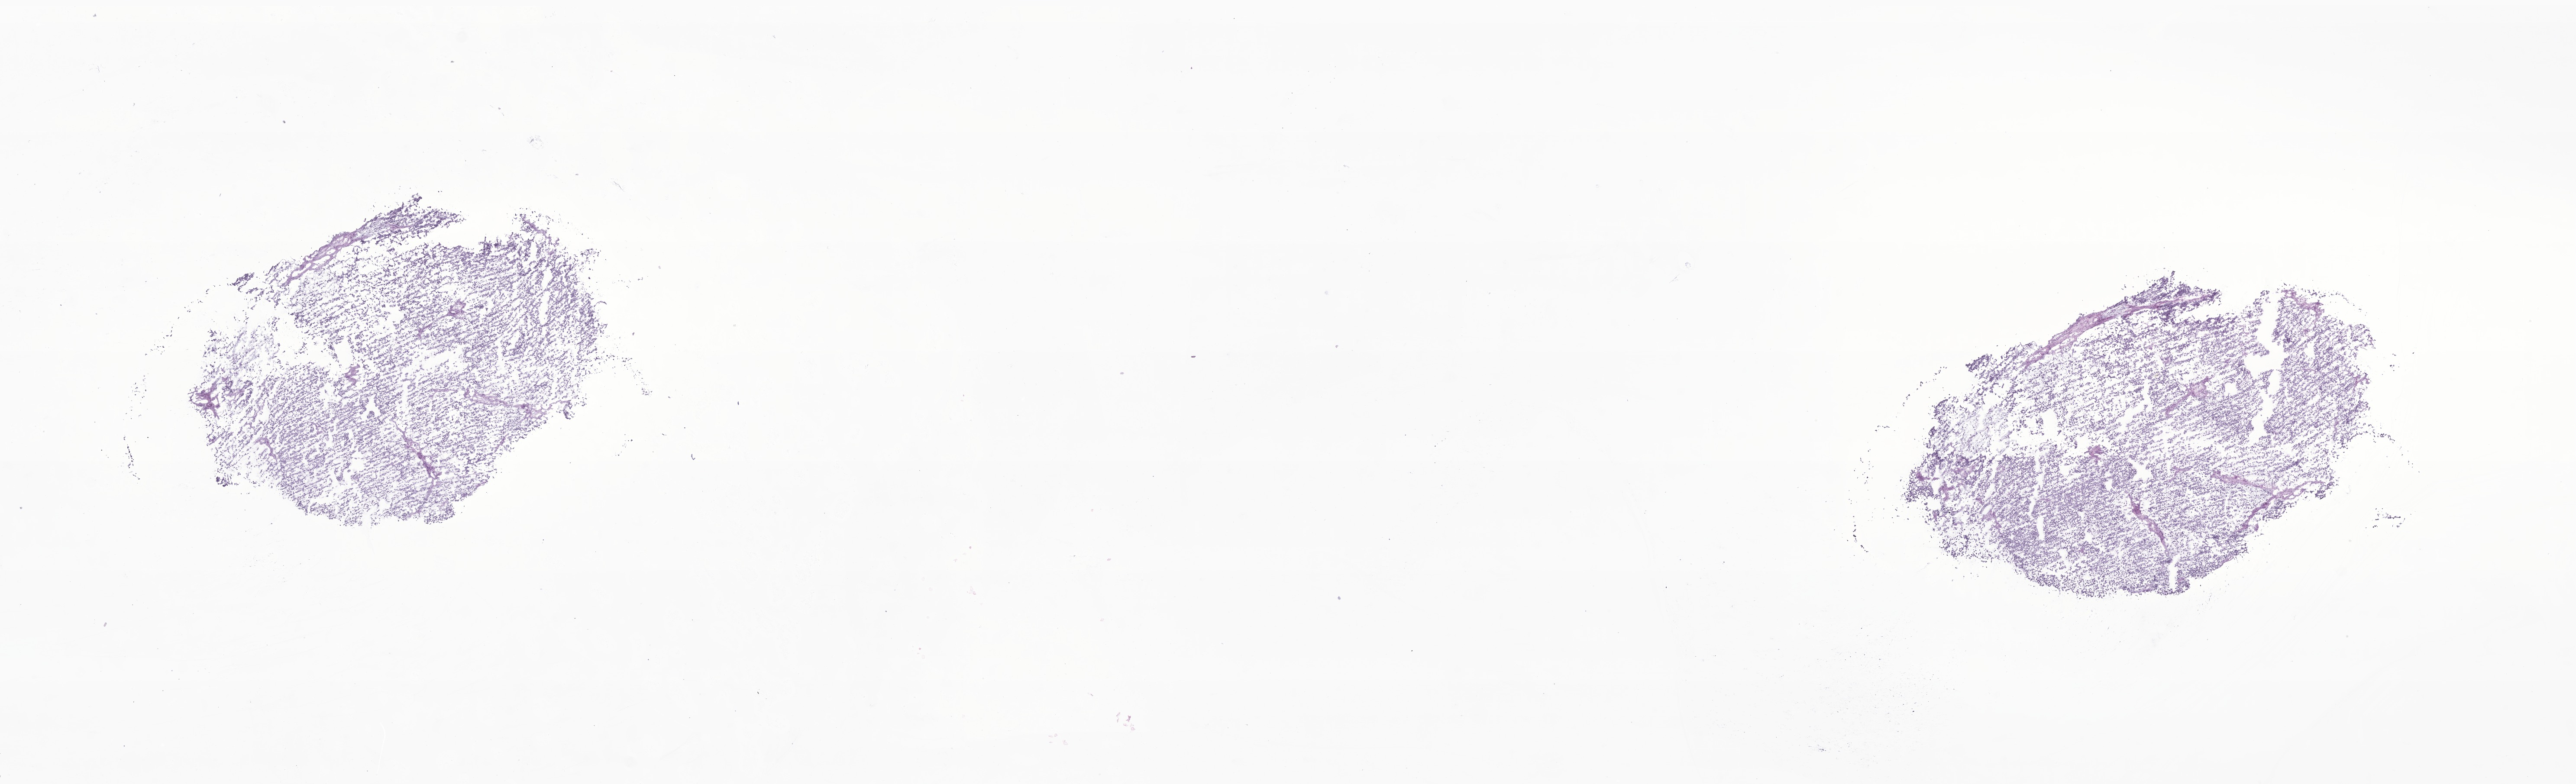
Haematoxylin and eosin whole-slide image of tumor tissue from the labium majus, shown as a low-resolution overview of the whole scanned area (about 25.1 x 7.6 mm). Cryosection (OCT / tissue freezing medium). Female patient, age 588 days.
• diagnosis (ICD-O-3 morphology term): Embryonal rhabdomyosarcoma, NOS